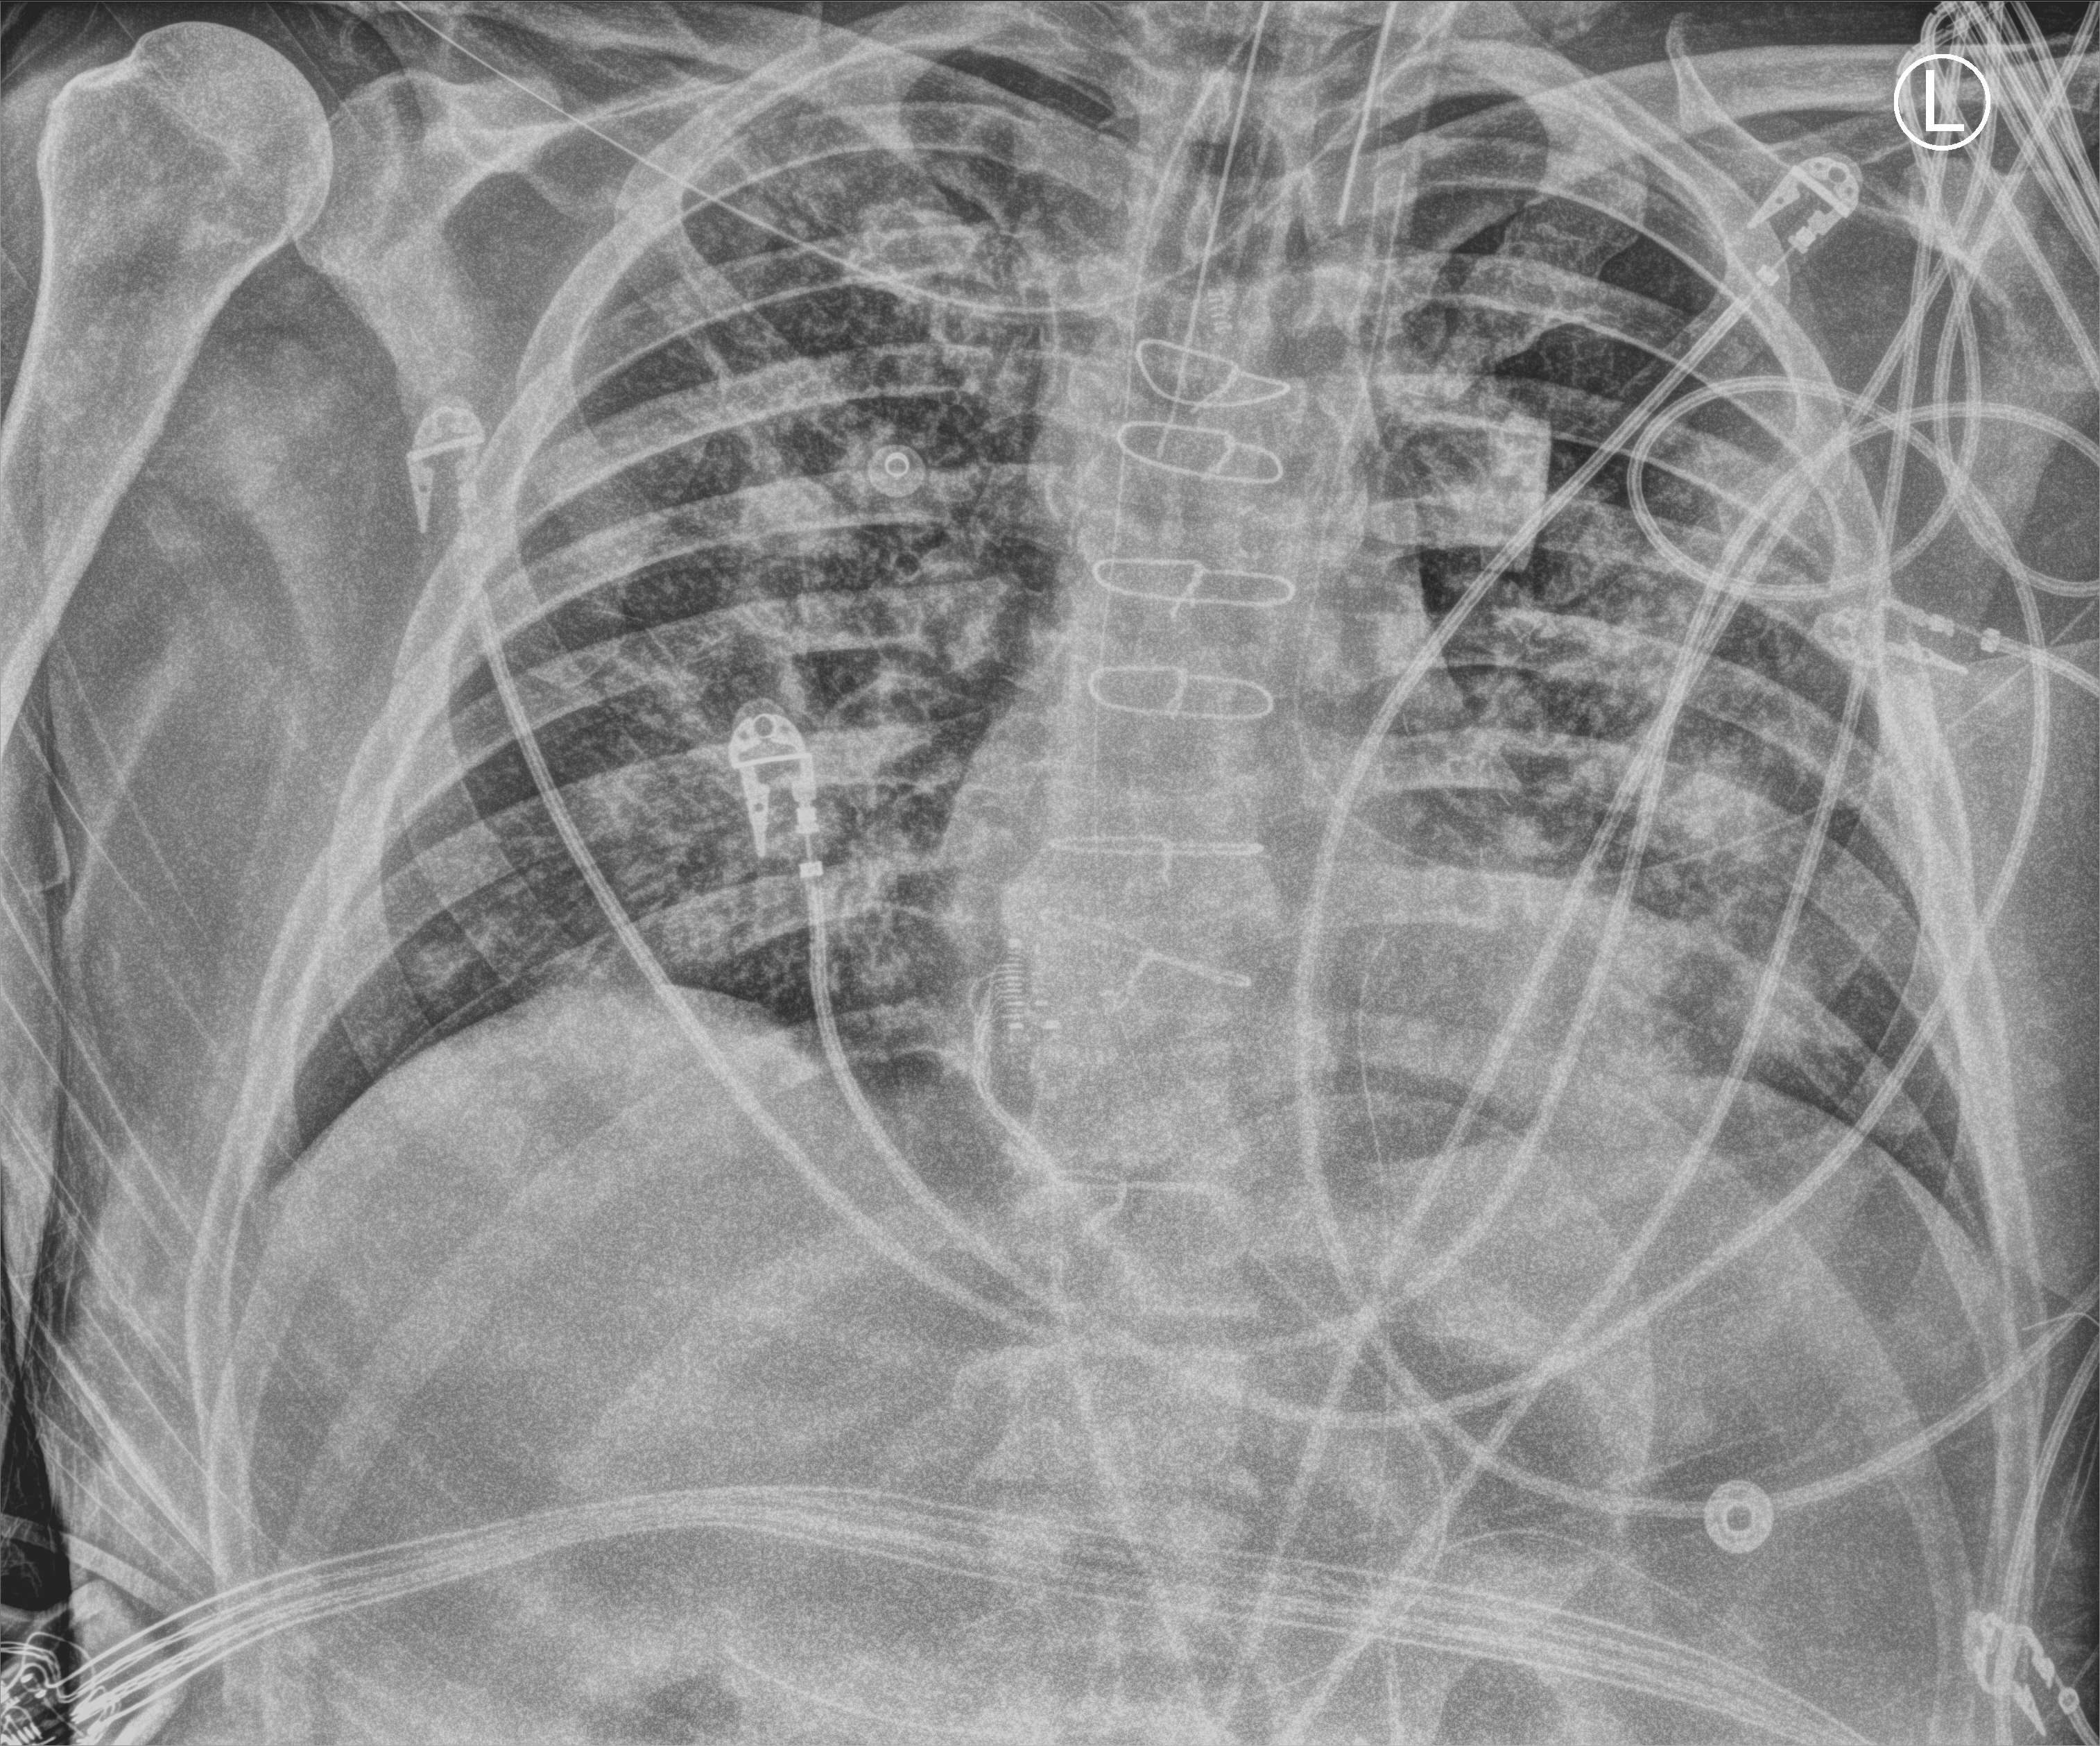
Chest X-ray (portable). Male patient hospitalised with COVID-19, age 60–74 years.
Admission-level facts for this patient (not findings on this image; timing relative to this image not recorded): length of hospital stay: 44 days; hypertension (admission record): yes; mechanically ventilated during this hospital stay: yes.